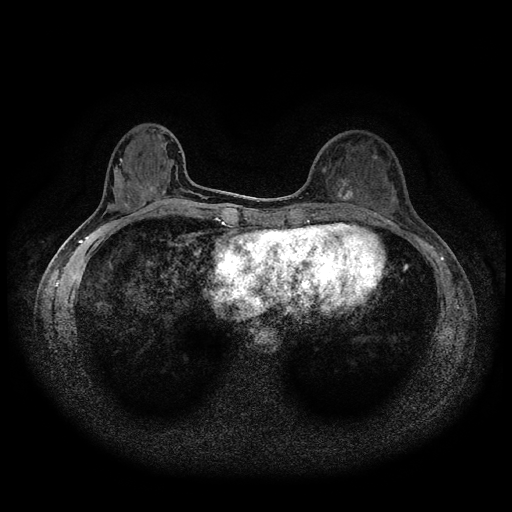
Breast MRI (dynamic contrast-enhanced, multi-phase), one axial slice. Slice 35 of 116 in the series (ordered by position). Dynamic contrast-enhanced series, time point 2 of 5 at this slice position (early post-contrast). 1.5 T. TE 2.7 ms, TR 5.4 ms. 2 mm slice thickness. 512 × 512 image matrix. Patient: female, 36 years.
Annotated regions visible in this slice (semi-automatic segmentation, software-assisted and operator-edited):
- breast lesion (labelled benign in the annotation): bounding box <335,177,357,203> (left, top, right, bottom; pixels)